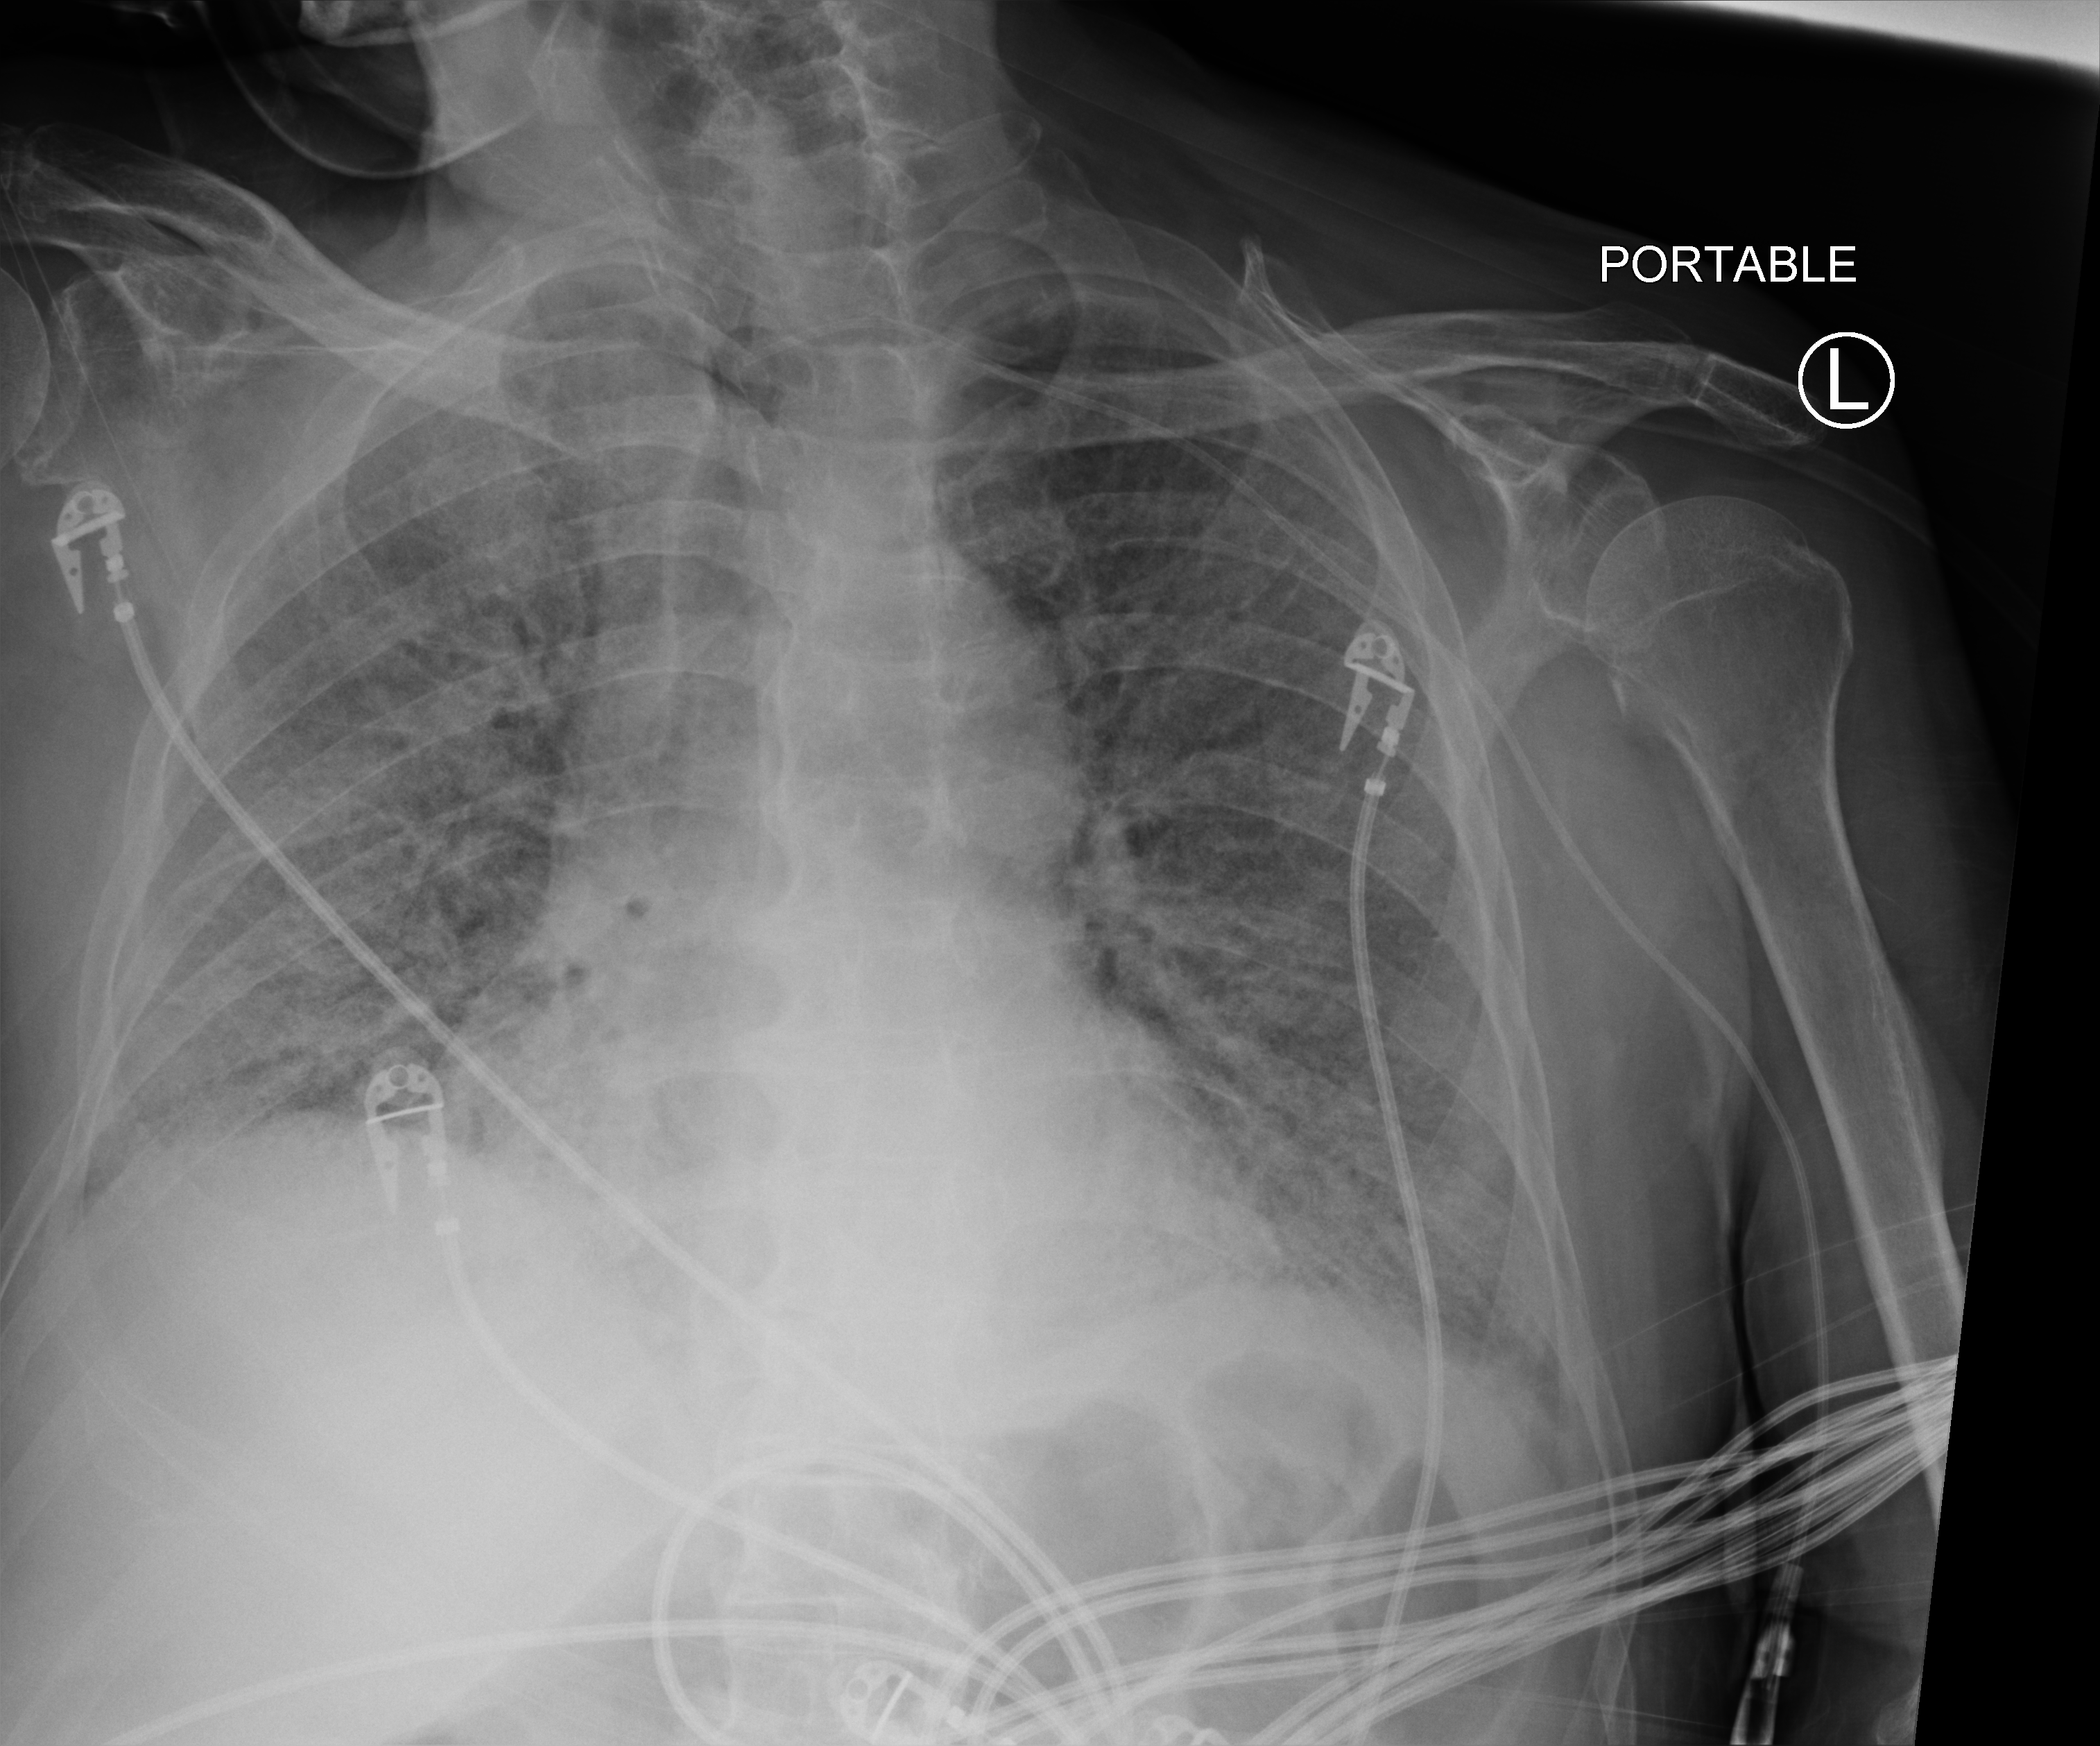
Bedside chest radiograph (computed radiography); anteroposterior (AP) projection. Male patient hospitalised with COVID-19, age 75–90 years.
From the hospital-stay record, not from the radiograph (when in the stay this image was taken is not recorded): admitted to intensive care during this hospital stay: yes; mechanically ventilated during this hospital stay: yes; chronic kidney disease (admission record): no.